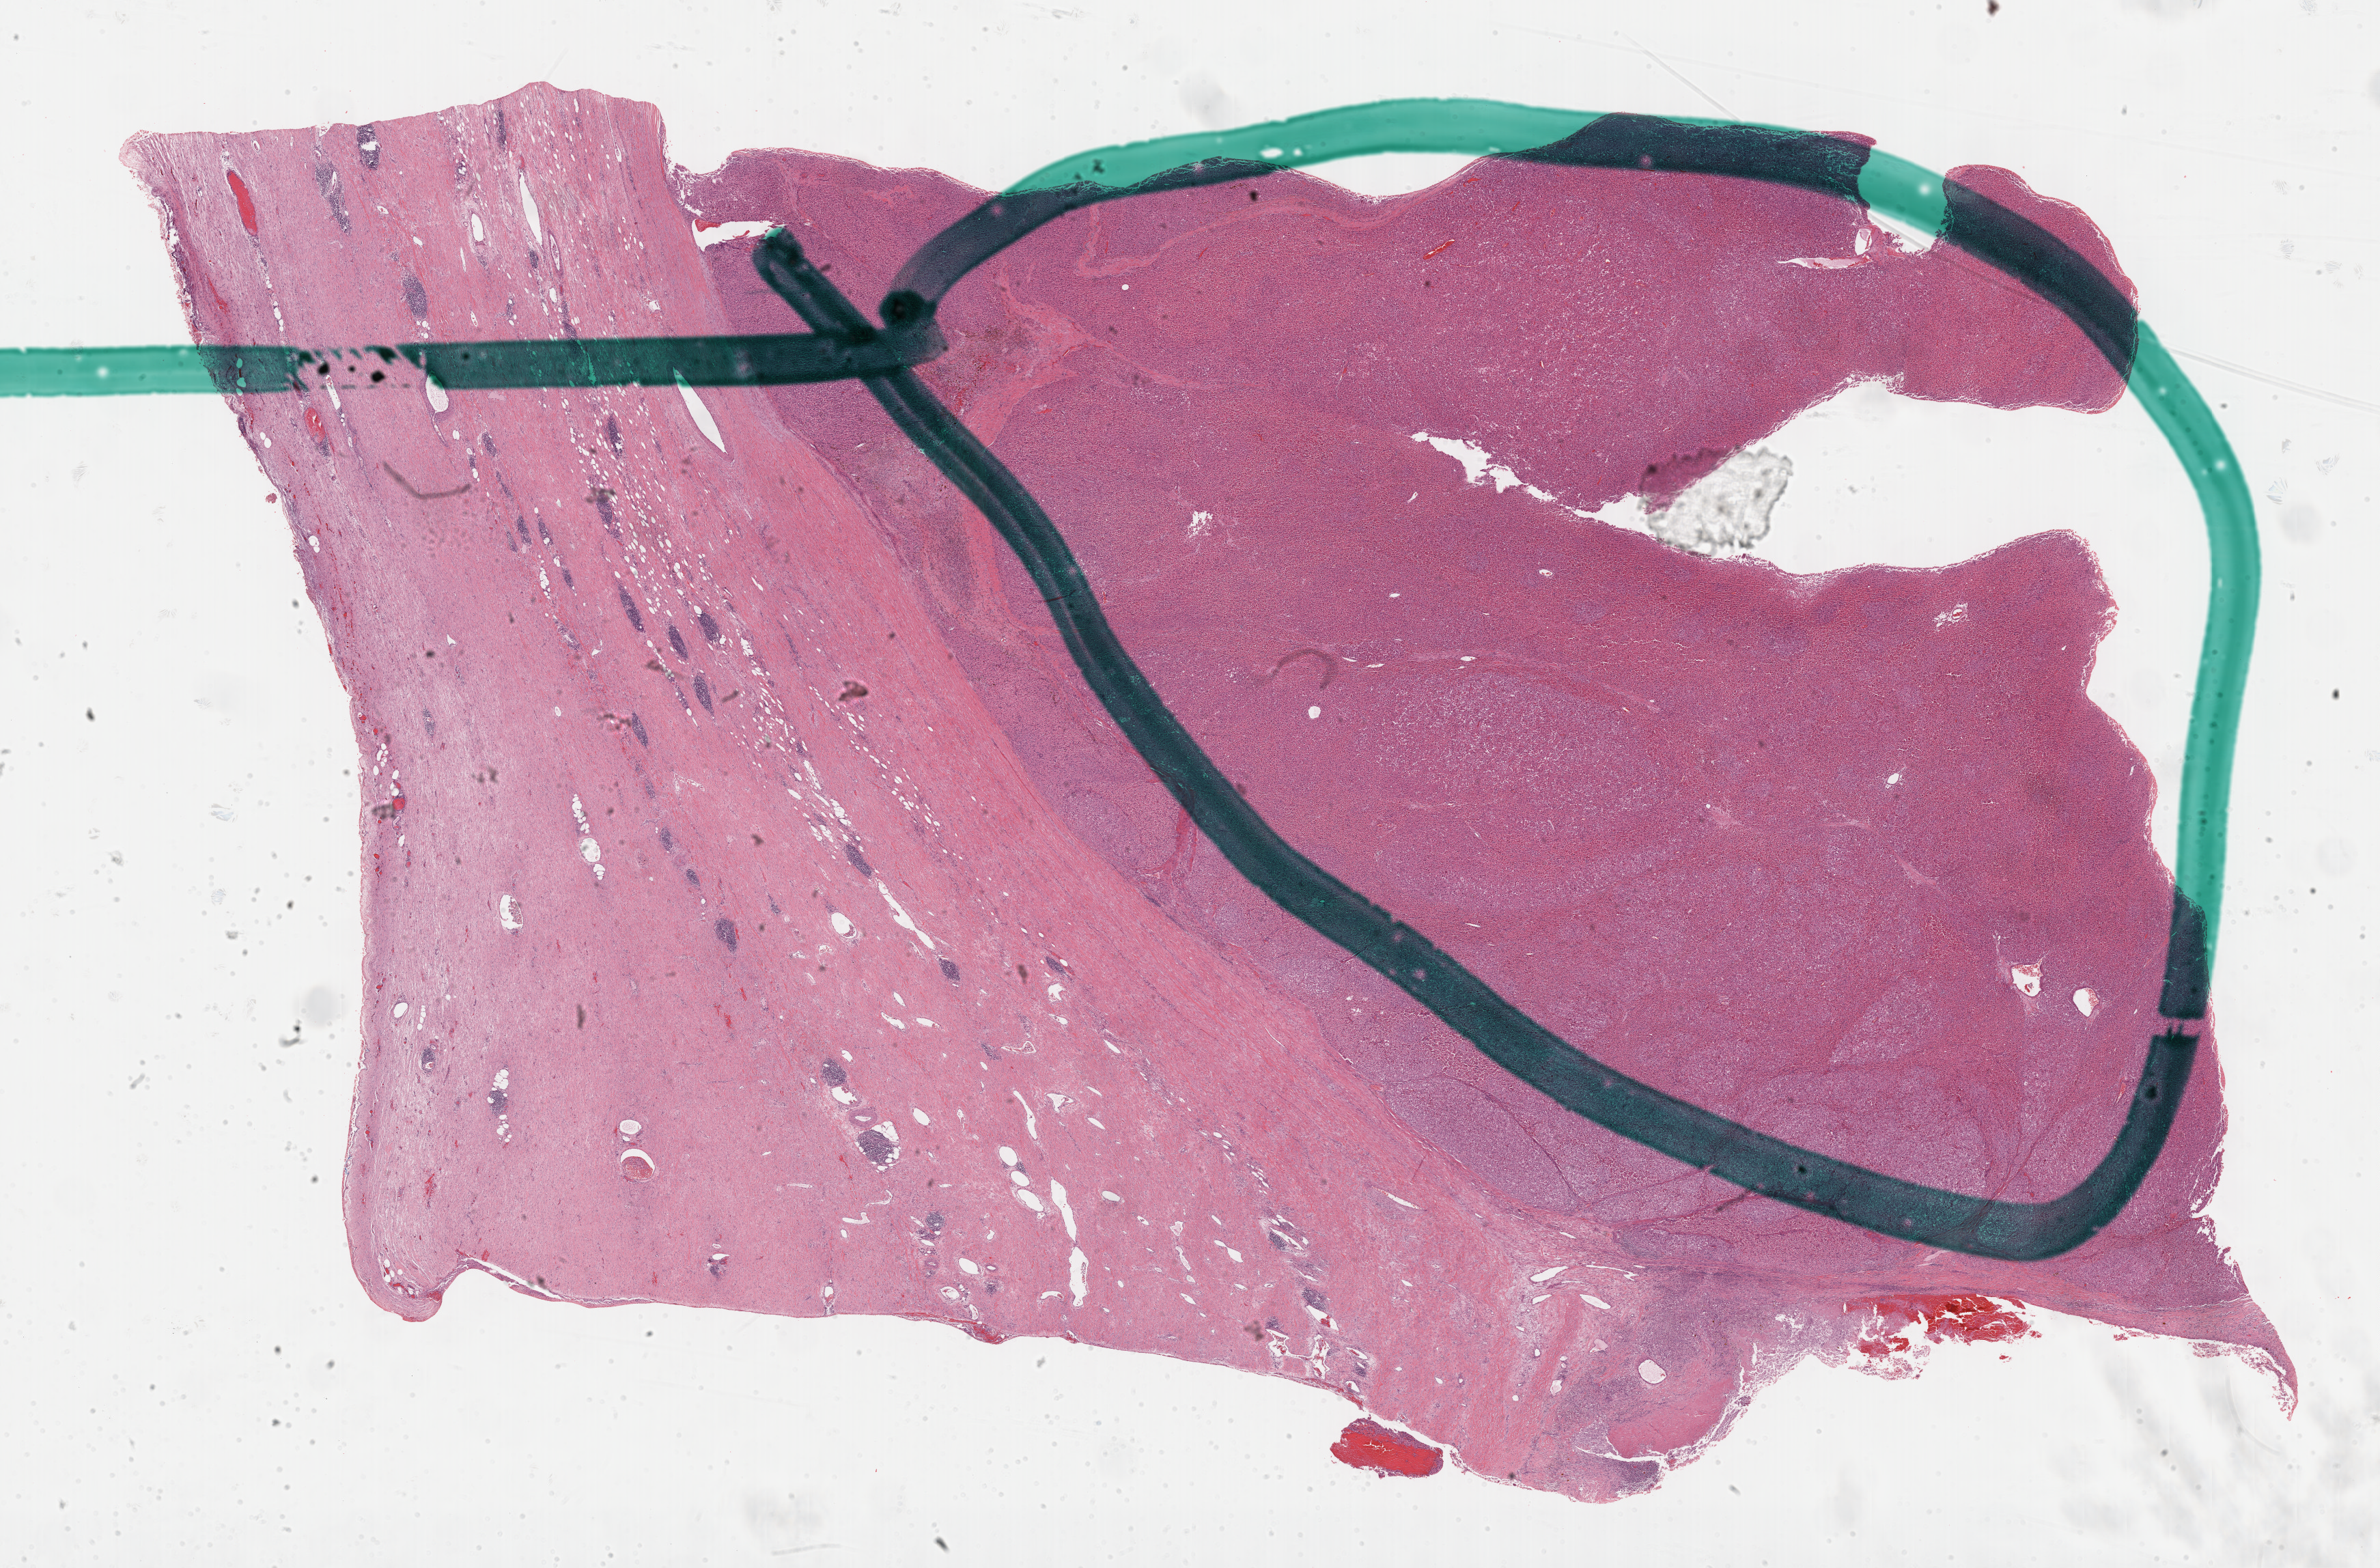
Whole-slide histology image, Hematoxylin and eosin (H&E) stained — low-resolution overview of the scanned area, about 28.2 x 18.6 mm; FFPE section; sample: primary tumour, adrenal cortex. Male patient; age at initial diagnosis 53 years.
Pathologic diagnosis: Adrenal cortical carcinoma (cortex of adrenal gland).